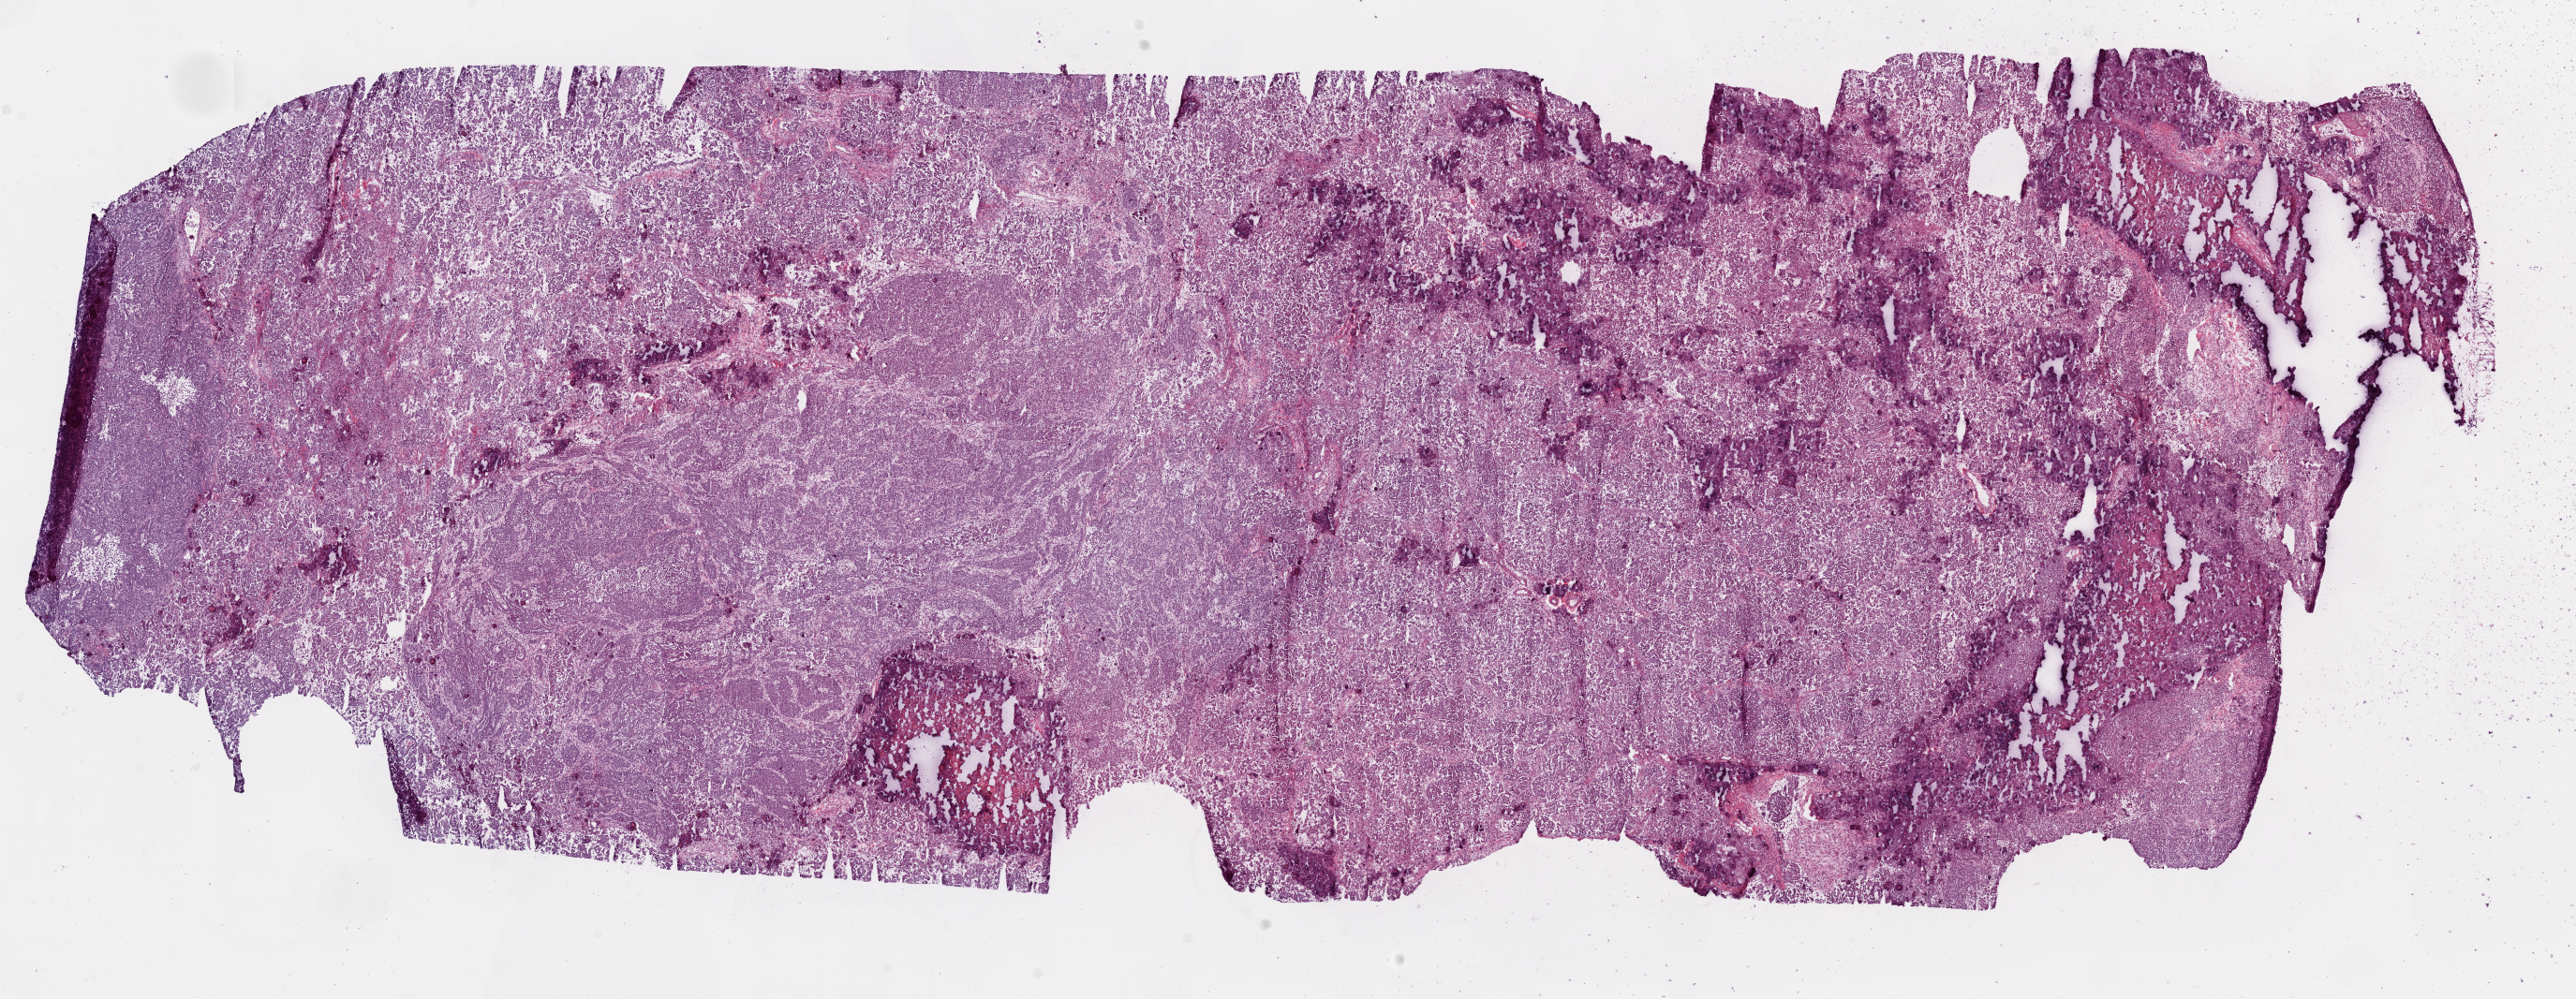
Digitized H&E-stained tissue section (whole slide), whole scanned area (about 22.1 x 8.6 mm, slide scanned at 20x) shown as a low-resolution overview. Frozen section. Primary tumour sample from the ovary. Female patient; age at initial diagnosis 57 years. Histologic grade: G2 (moderately differentiated). Pathologist review of this section (percent, as recorded): tumour cells 75%, tumour nuclei 85%, normal cells 0%, stromal cells 5%, necrosis 20%.
Laterality: bilateral. FIGO stage: IV. Pathologic diagnosis: Serous cystadenocarcinoma, NOS.